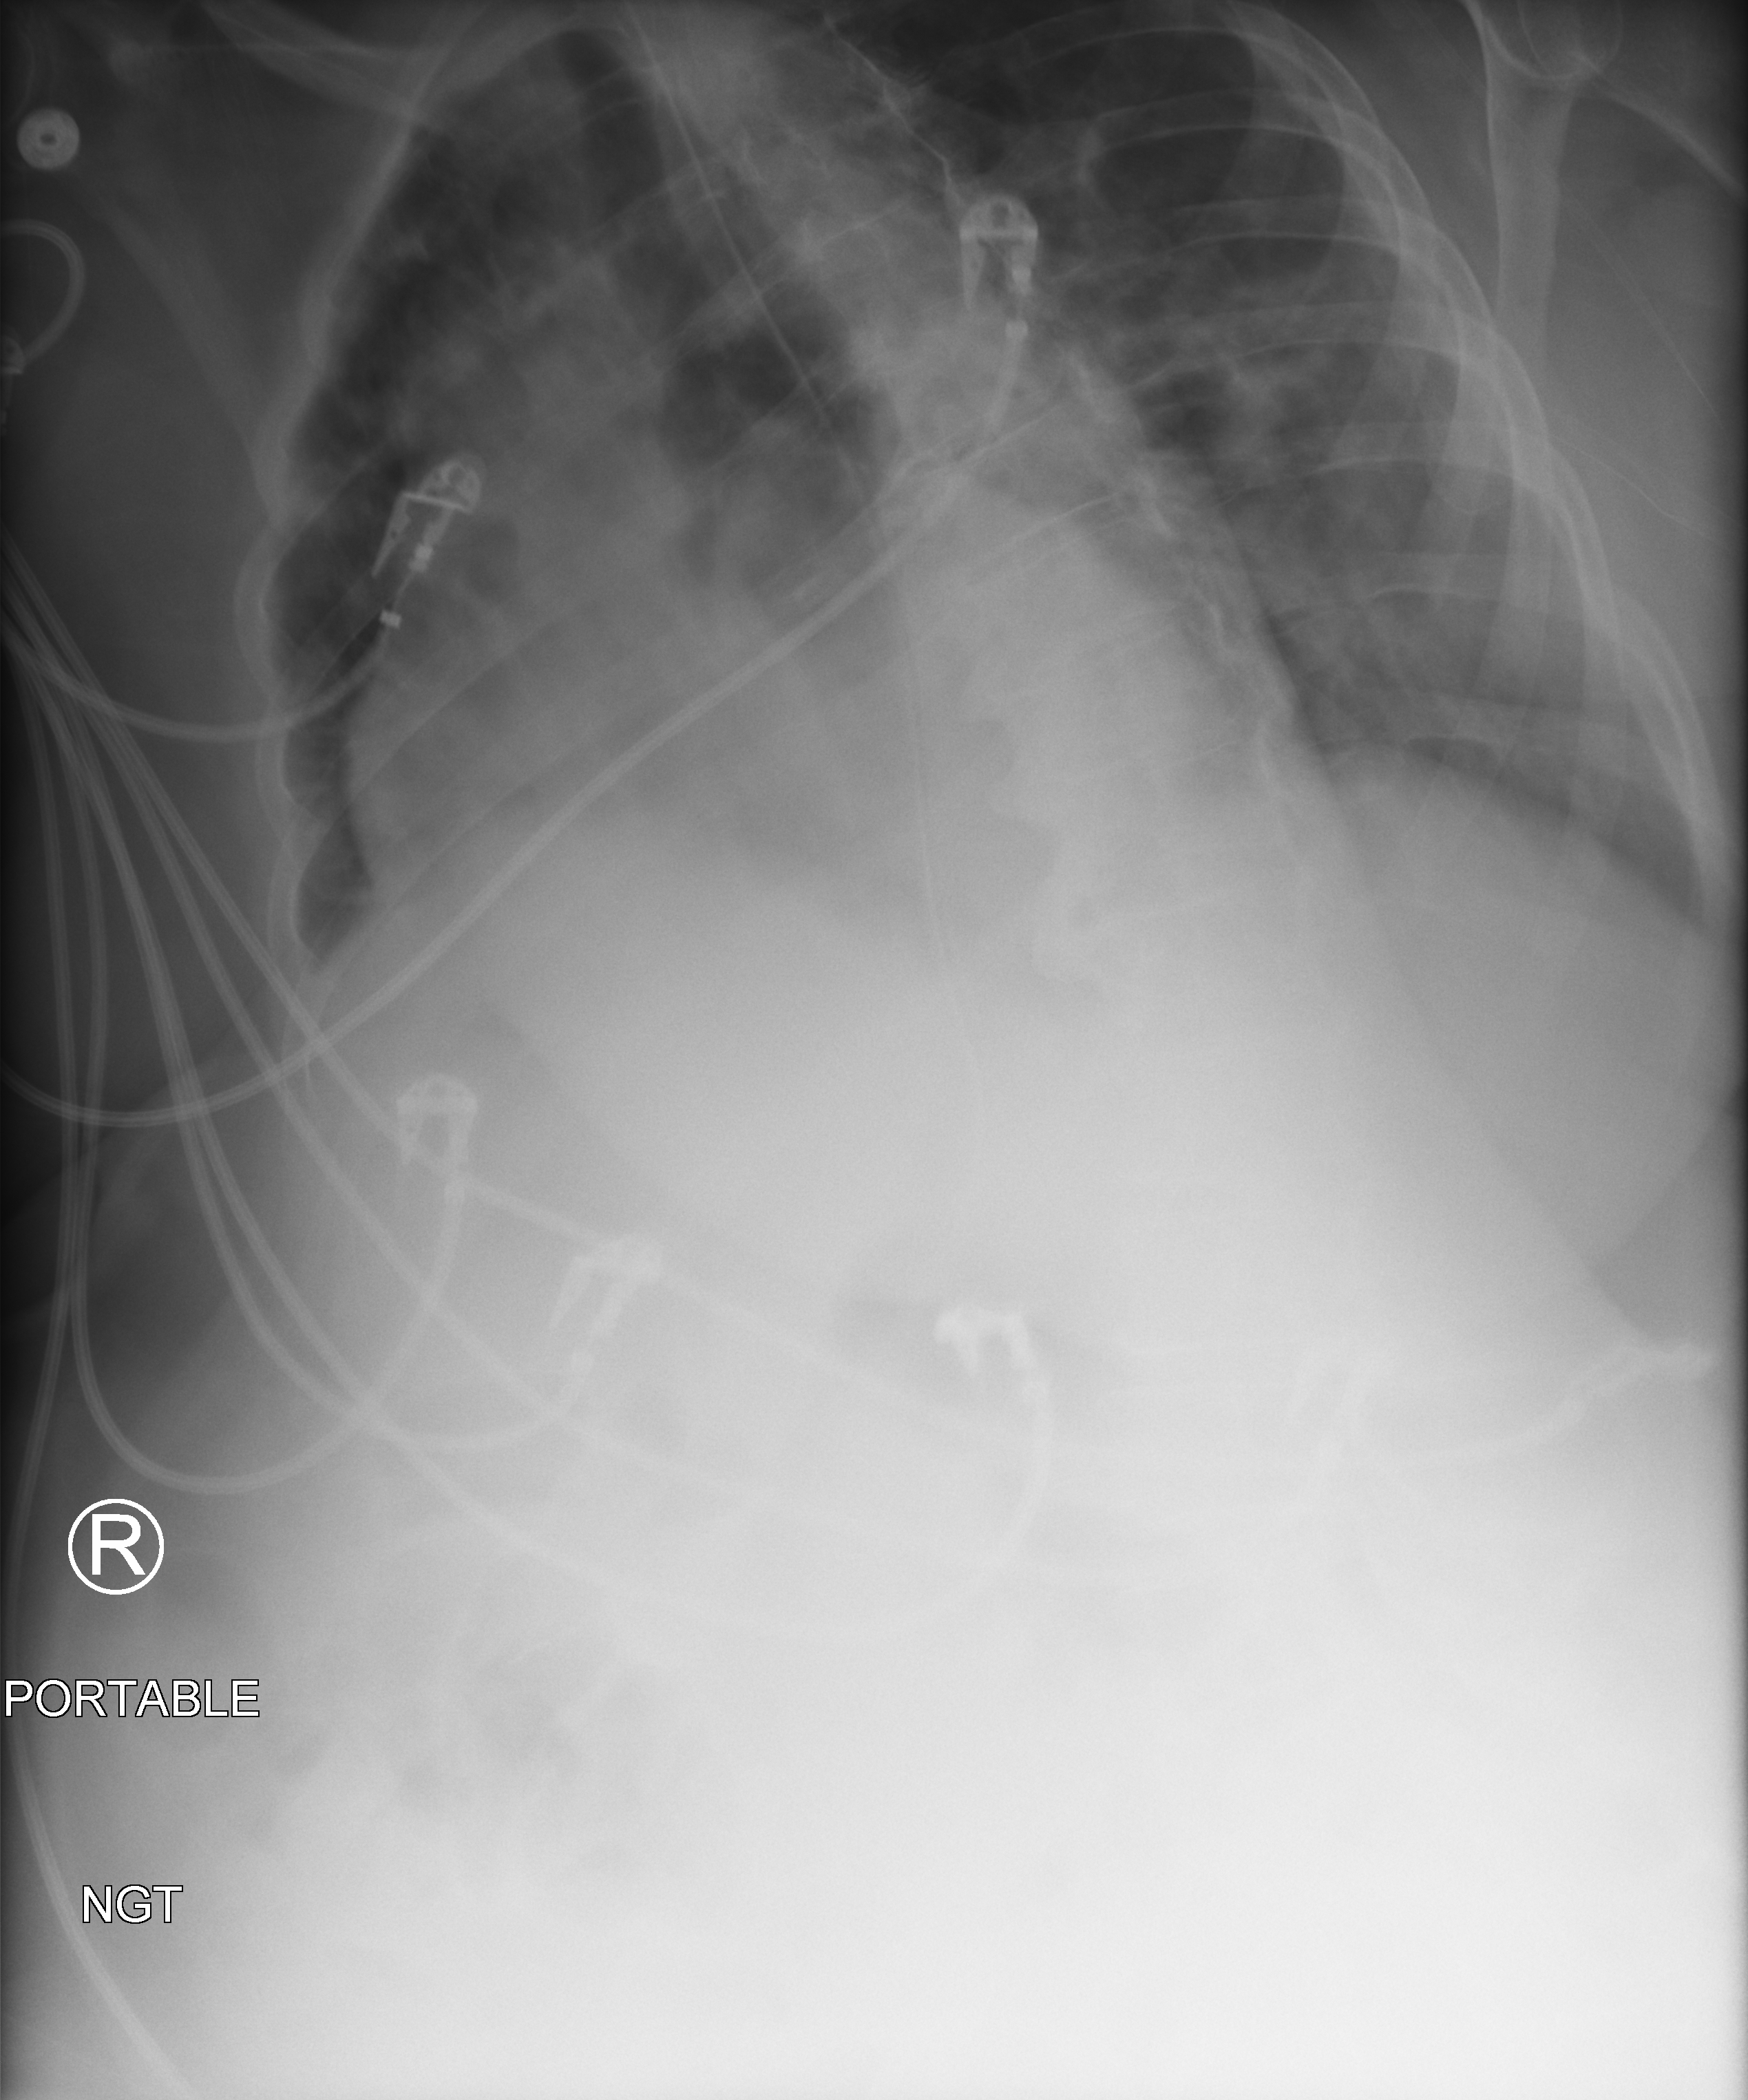
Abdomen radiograph (computed radiography). Female patient hospitalised with COVID-19, age 75–90 years.
Admission-level facts for this patient (not findings on this image; timing relative to this image not recorded):
- other chronic lung disease (admission record): yes
- COPD (admission record): yes
- admitted to intensive care during this hospital stay: yes